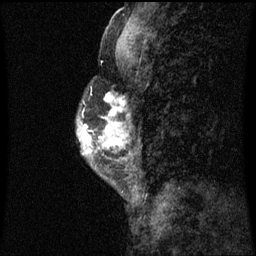
Breast MRI (dynamic contrast-enhanced), one sagittal slice; position 21 of 60 along the scan axis; dynamic contrast-enhanced series, image 2 of 3 at this slice position (ordered by acquisition); 1.5 T; TE 4.2 ms, TR 8.9 ms; 2 mm slice thickness; 256 × 256 image matrix, field of view 200 × 200 mm. Female patient, age 50 years. Case-level facts recorded for this patient, not image findings: setting: breast cancer imaged before/during neoadjuvant chemotherapy; receptor status: triple-negative.
Outlined on this slice (semi-automatically segmented with operator editing):
- analysis volume of interest (the breast-tissue region the enhancement analysis was run in; not a lesion): bounding box [x1, y1, x2, y2] px = [77, 86, 116, 169]
- tumour enhancement mask (voxels above the 70 % enhancement threshold inside the analysis volume of interest): [85, 94, 116, 149]